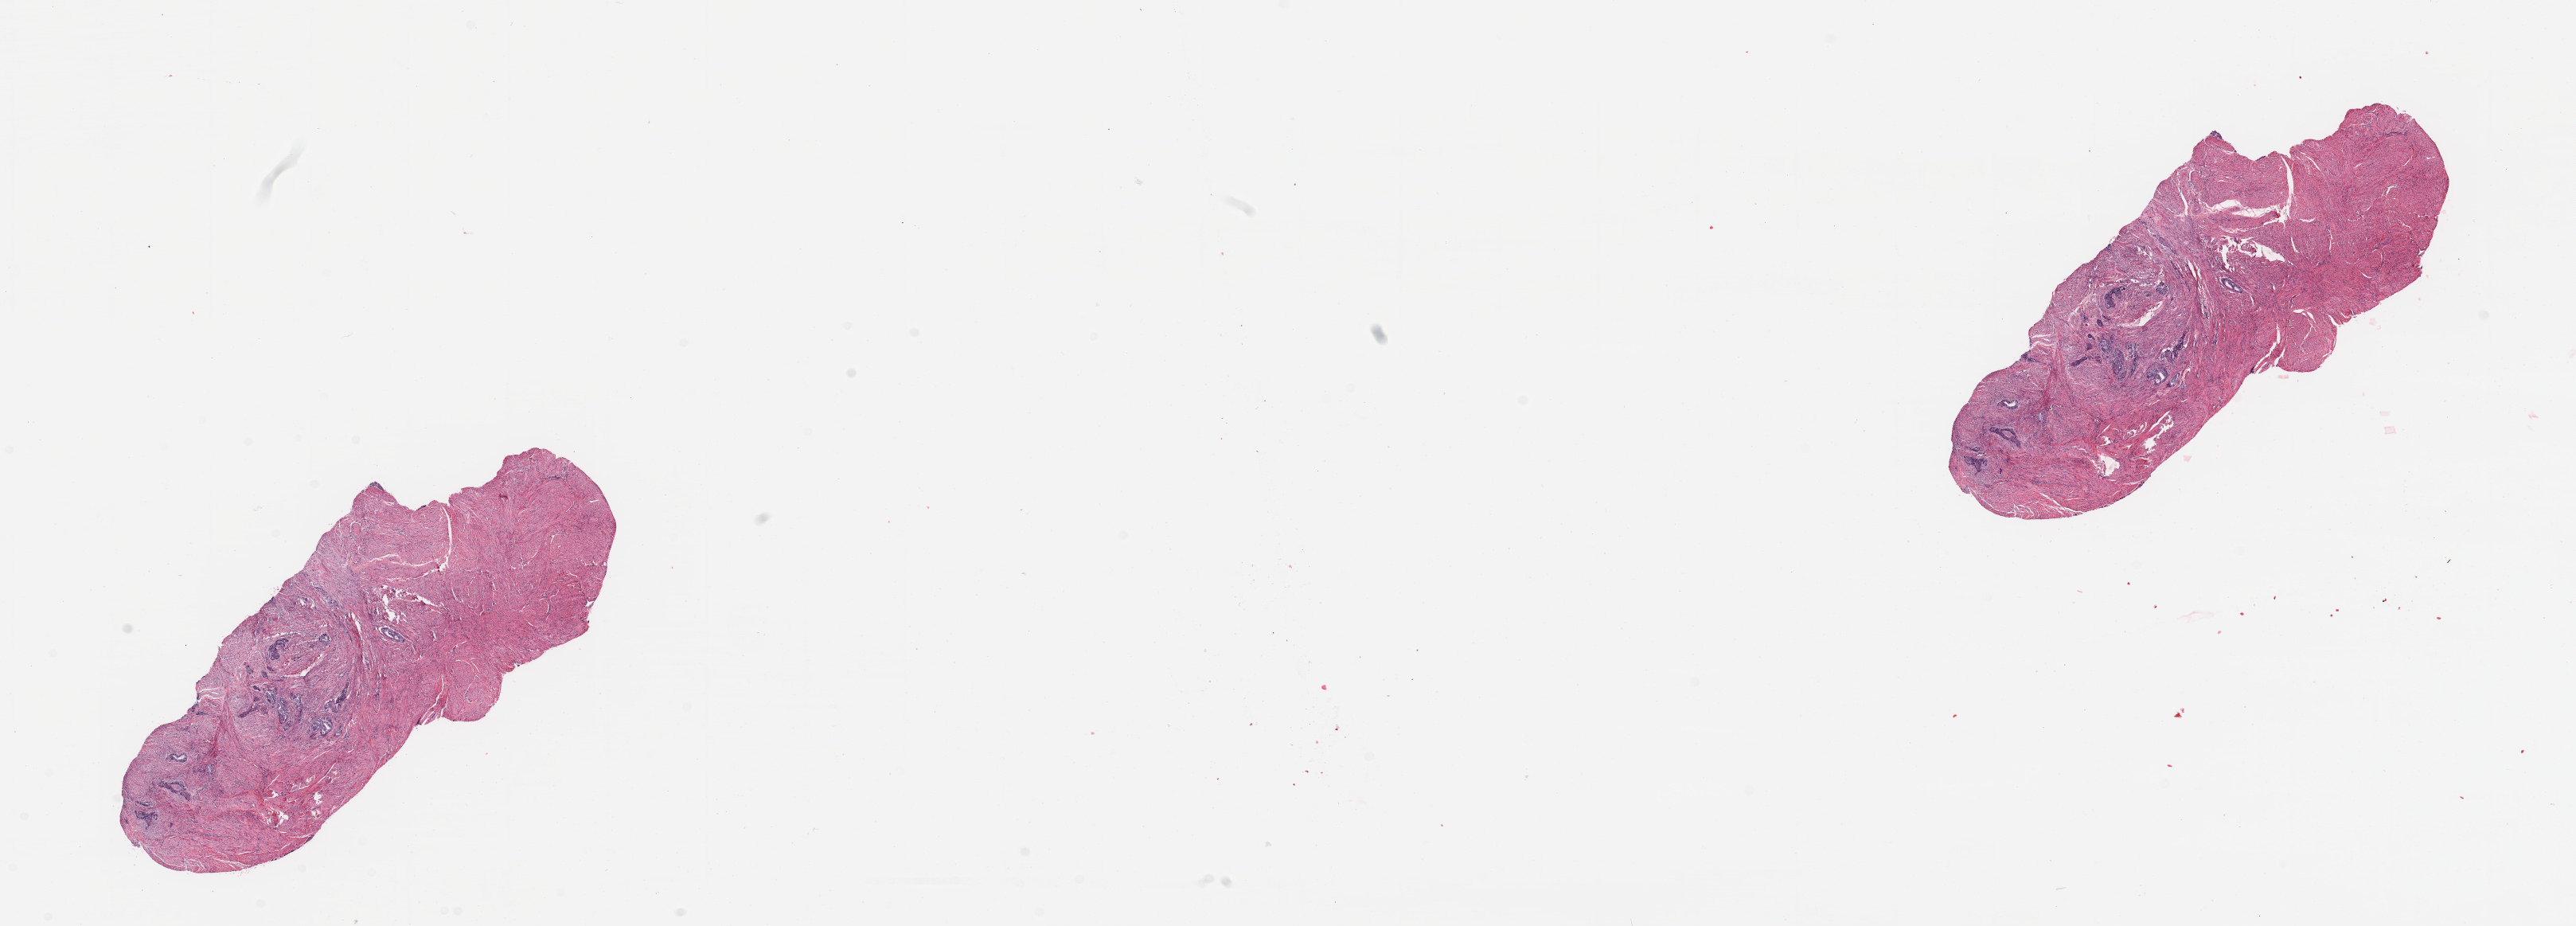
Whole-slide histology image, Hematoxylin and eosin (H&E) stained — whole scanned area (about 25.6 x 9.2 mm, acquisition: 20x scan) shown as a low-resolution overview; uterus, normal (non-tumour) tissue. Female, 61 y/o.
This section: normal (non-tumour) tissue from the same patient. Patient diagnosis: Endometrioid adenocarcinoma, NOS.